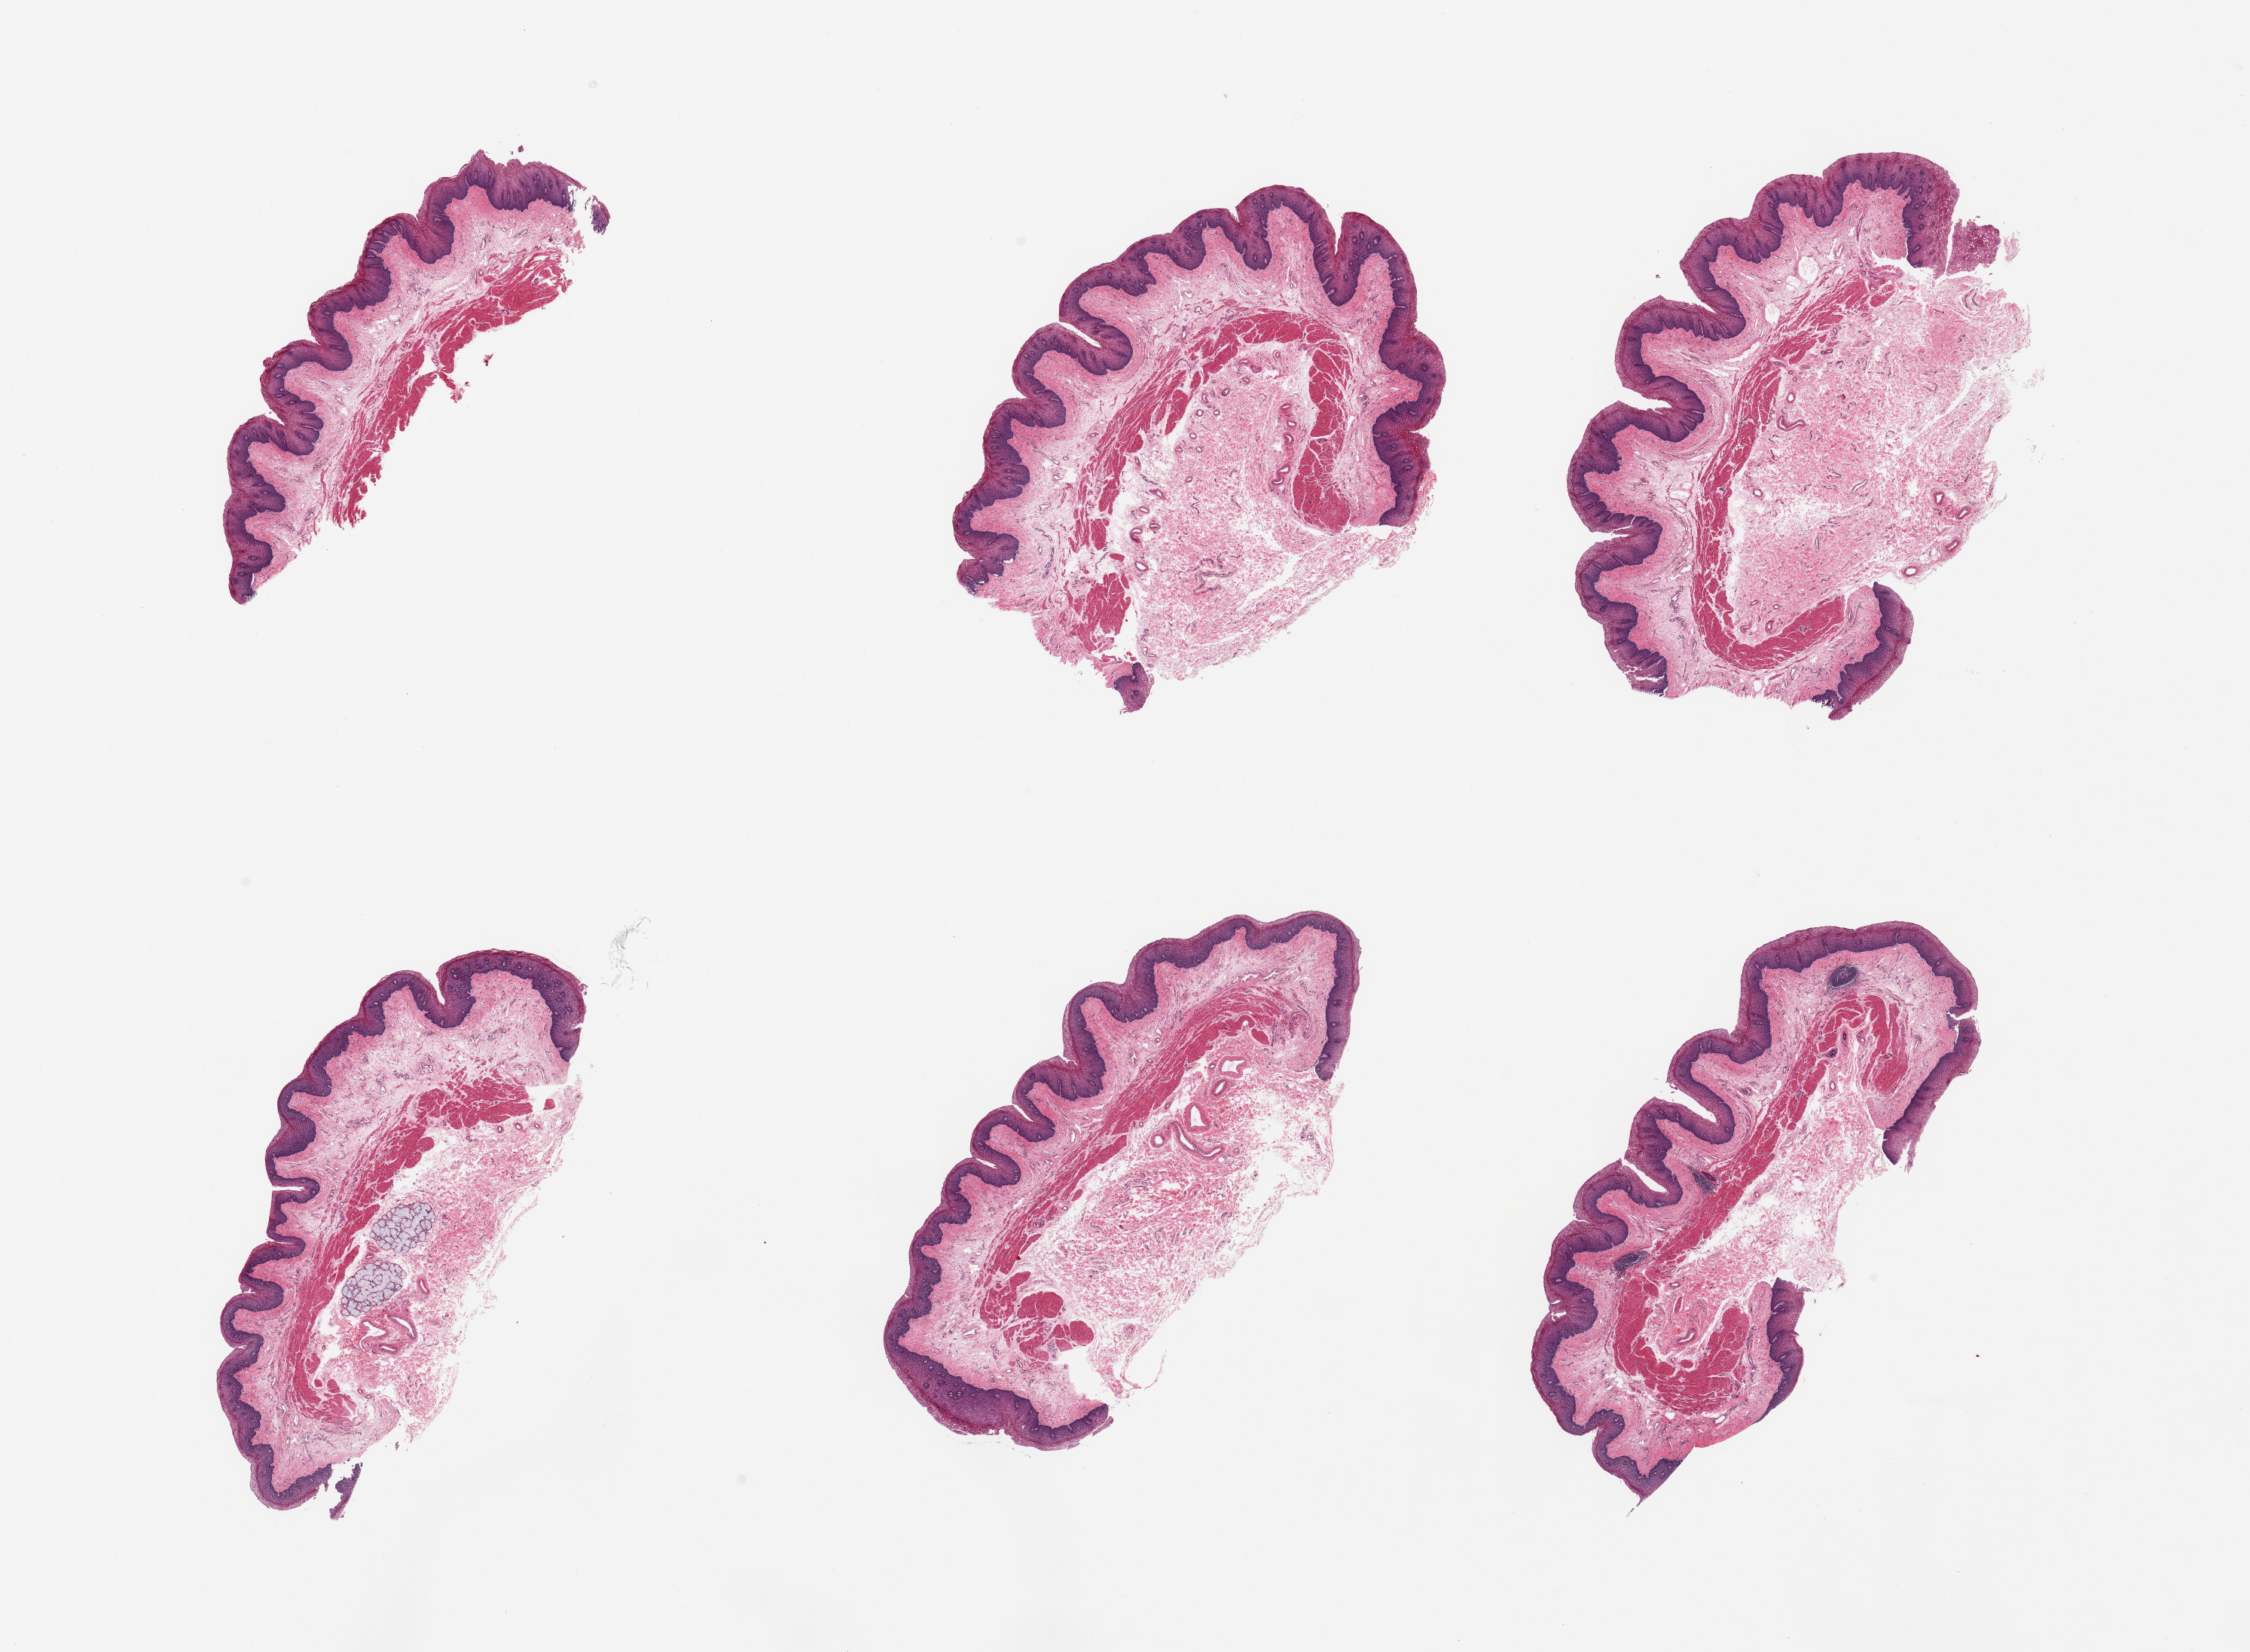
Whole-slide image, hematoxylin and eosin (H&E) stain, whole scanned area (about 23.6 x 17.3 mm, slide scanned at 20x) shown as a low-resolution overview, PAXgene-fixed, paraffin-embedded tissue, target tissue: esophageal mucous membrane, donor tissue sample. Donor: female.
Reviewer comment on this tissue sample: 2 pieces, squamous mucosa up to ~0.3mm; incidental submucosal mucus glands noted.